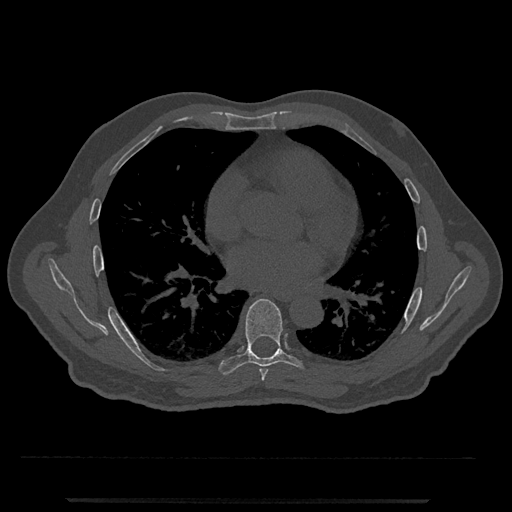
CT including the spine, one axial slice; position 691 of 797 along the scan axis; reconstruction kernel Br40s/3; 120 kVp; bone window (W 1800 / L 400 HU); 0.5 mm slice thickness; 512 × 512 image matrix, field of view 419 × 419 mm. Male patient, age 63 years. Case-level facts recorded for this patient, not image findings: primary cancer: prostate.
Structures marked on this image (semi-automatic segmentation, software-assisted and operator-edited):
- T6 vertebra: bounding box <259,369,268,381> (left, top, right, bottom; pixels)
- T7 vertebra: <218,299,304,375>